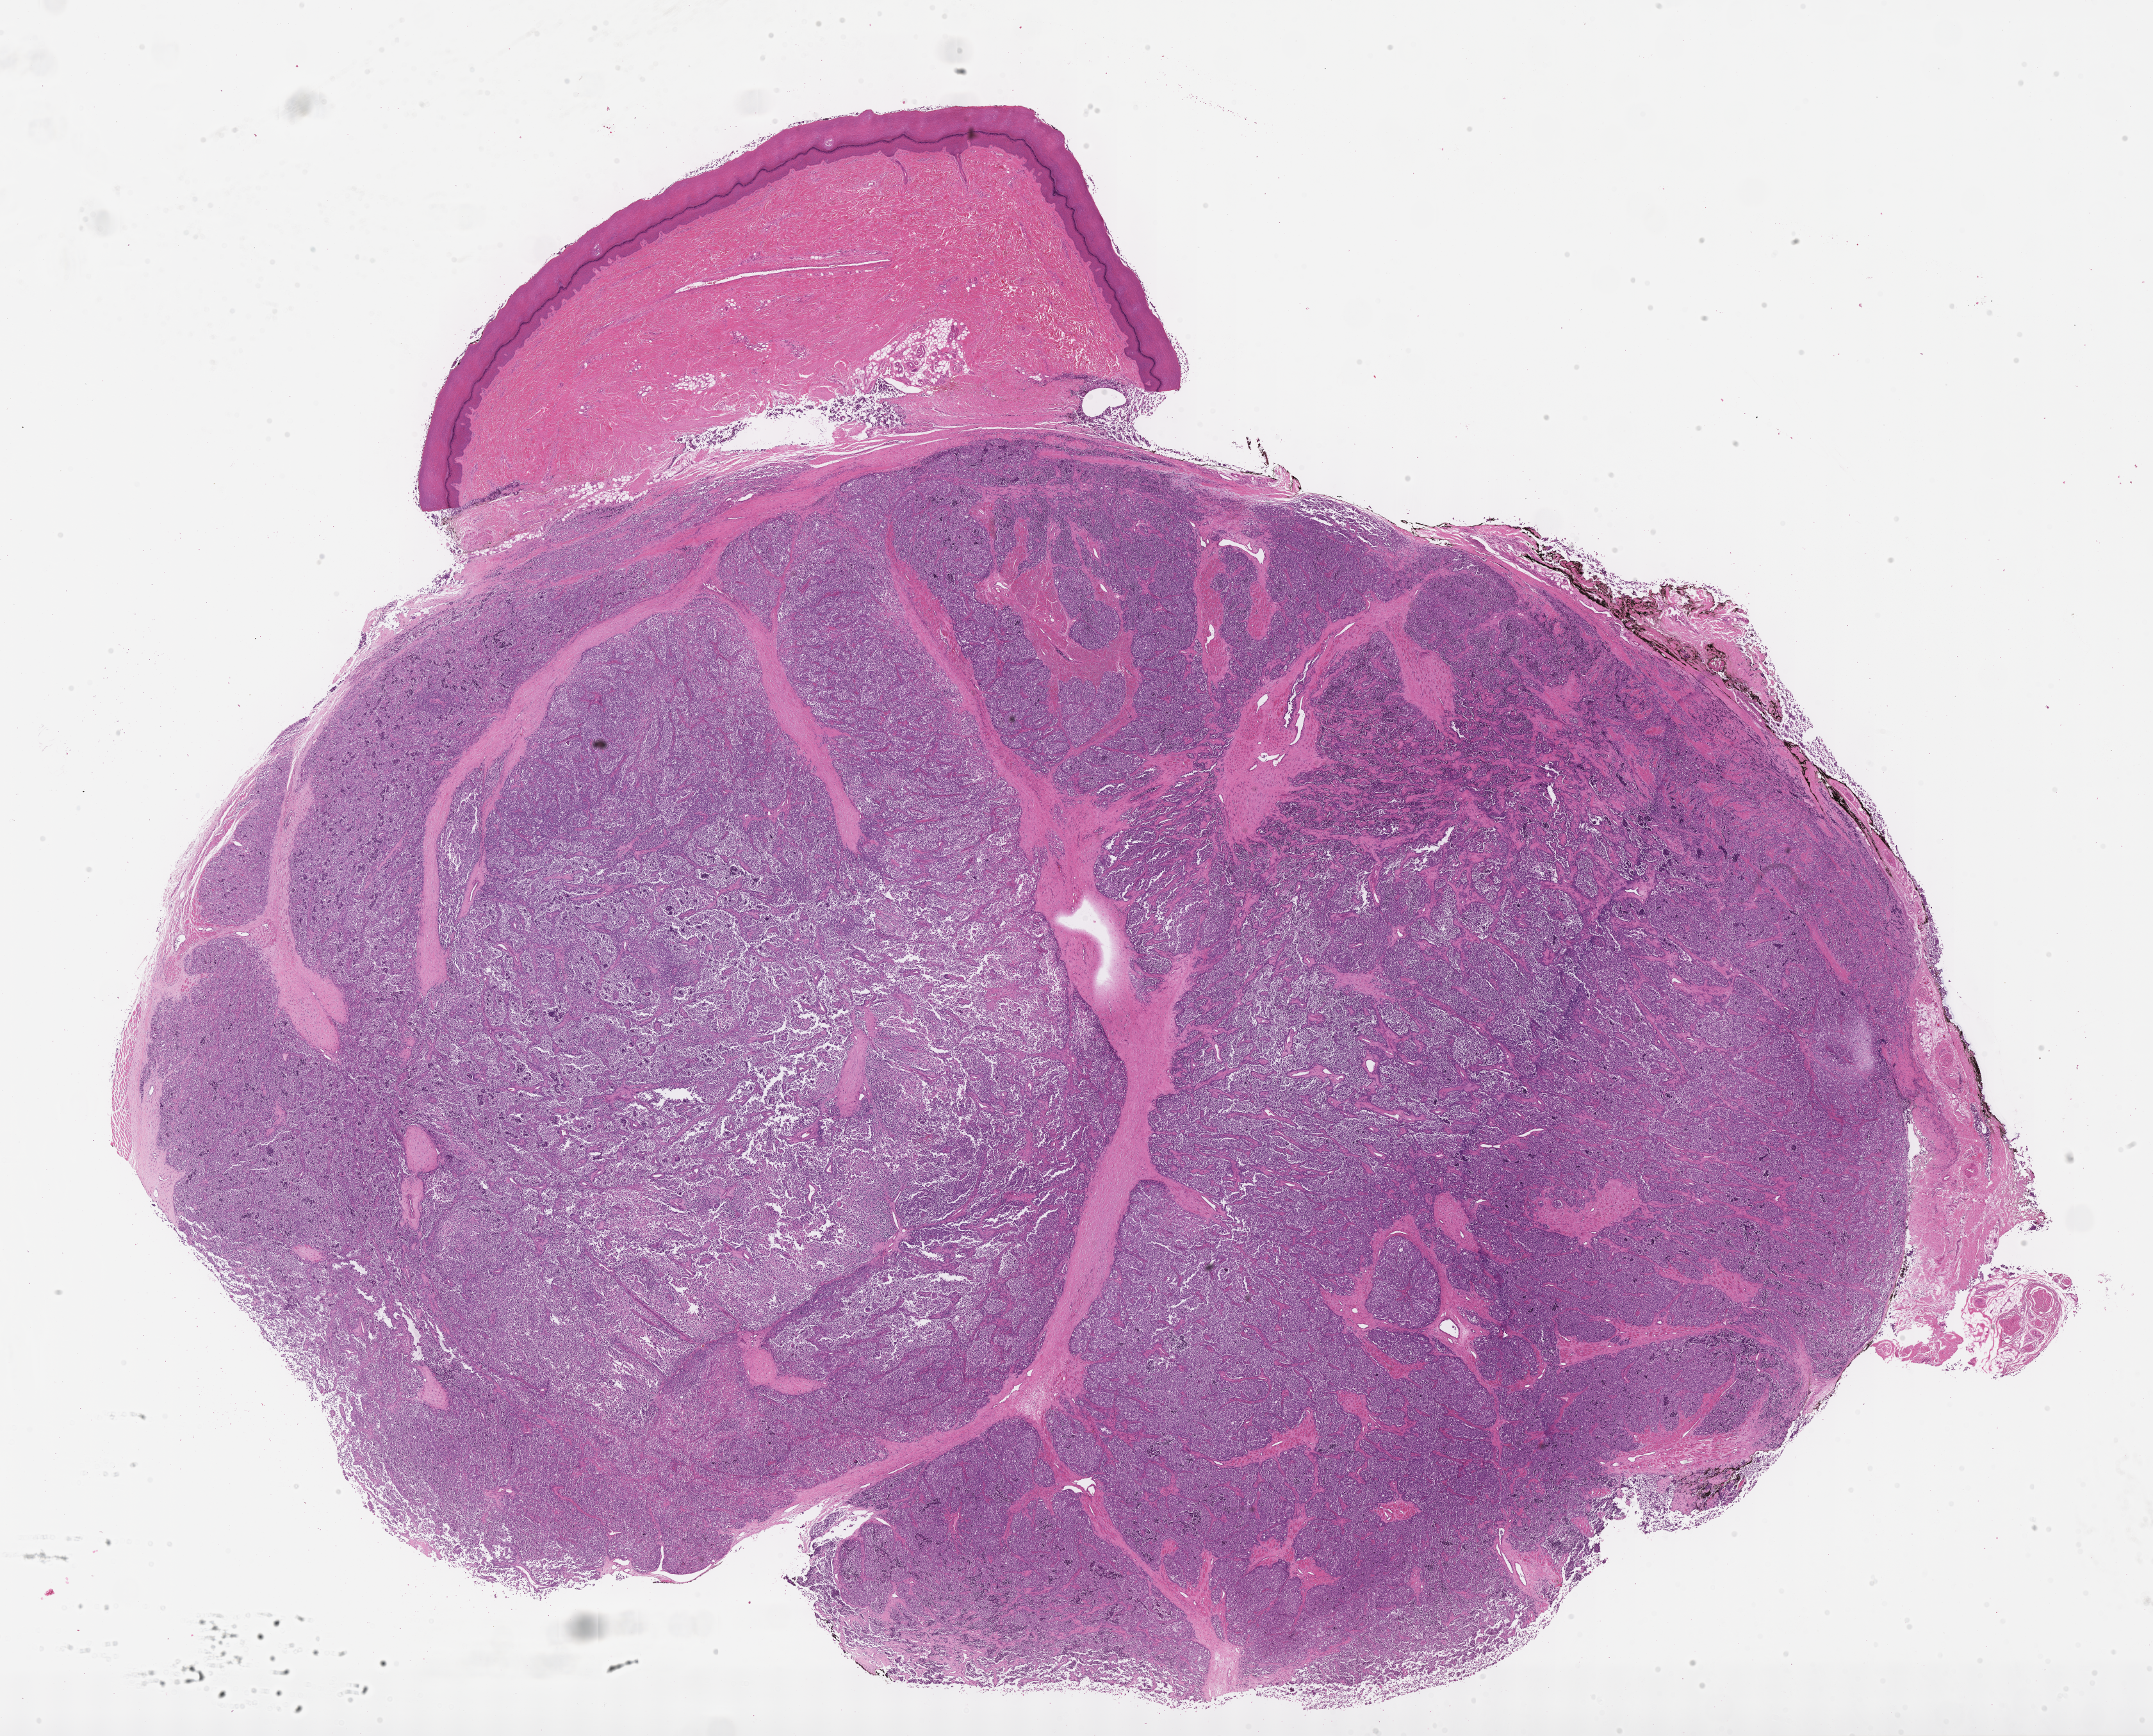
Haematoxylin and eosin whole-slide image of tumor tissue — a low-resolution overview of the entire scanned area, about 27.2 x 21.9 mm; formalin-fixed, paraffin-embedded (FFPE) tissue; sample anatomic site: foot, left. Male patient, age at diagnosis 15.2 years.
Stage (as recorded): 3. Metastatic status at presentation (as recorded): non-metastatic. Diagnosis: rhabdomyosarcoma; histological classification: alveolar rhabdomyosarcoma.